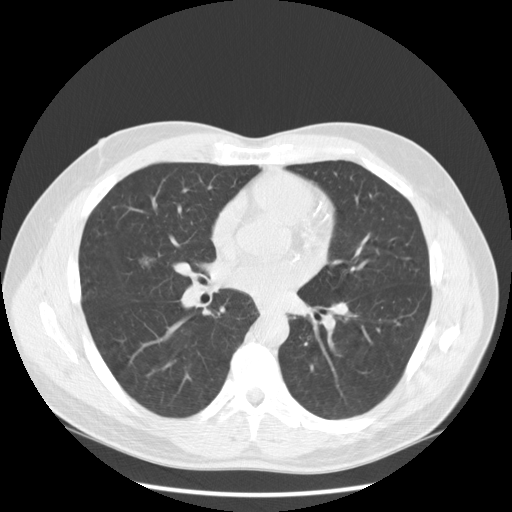
Low-dose screening chest CT, one axial slice. Position 111 of 234 along the scan axis. Lung window (W 1500 / L -600 HU). 512 × 512 image matrix, field of view 385 × 385 mm.
Structures marked on this image (manually delineated by an expert):
- lesion 1 (tumor, middle lobe of right lung): bounding box [x1, y1, x2, y2] px = [139, 254, 155, 268]